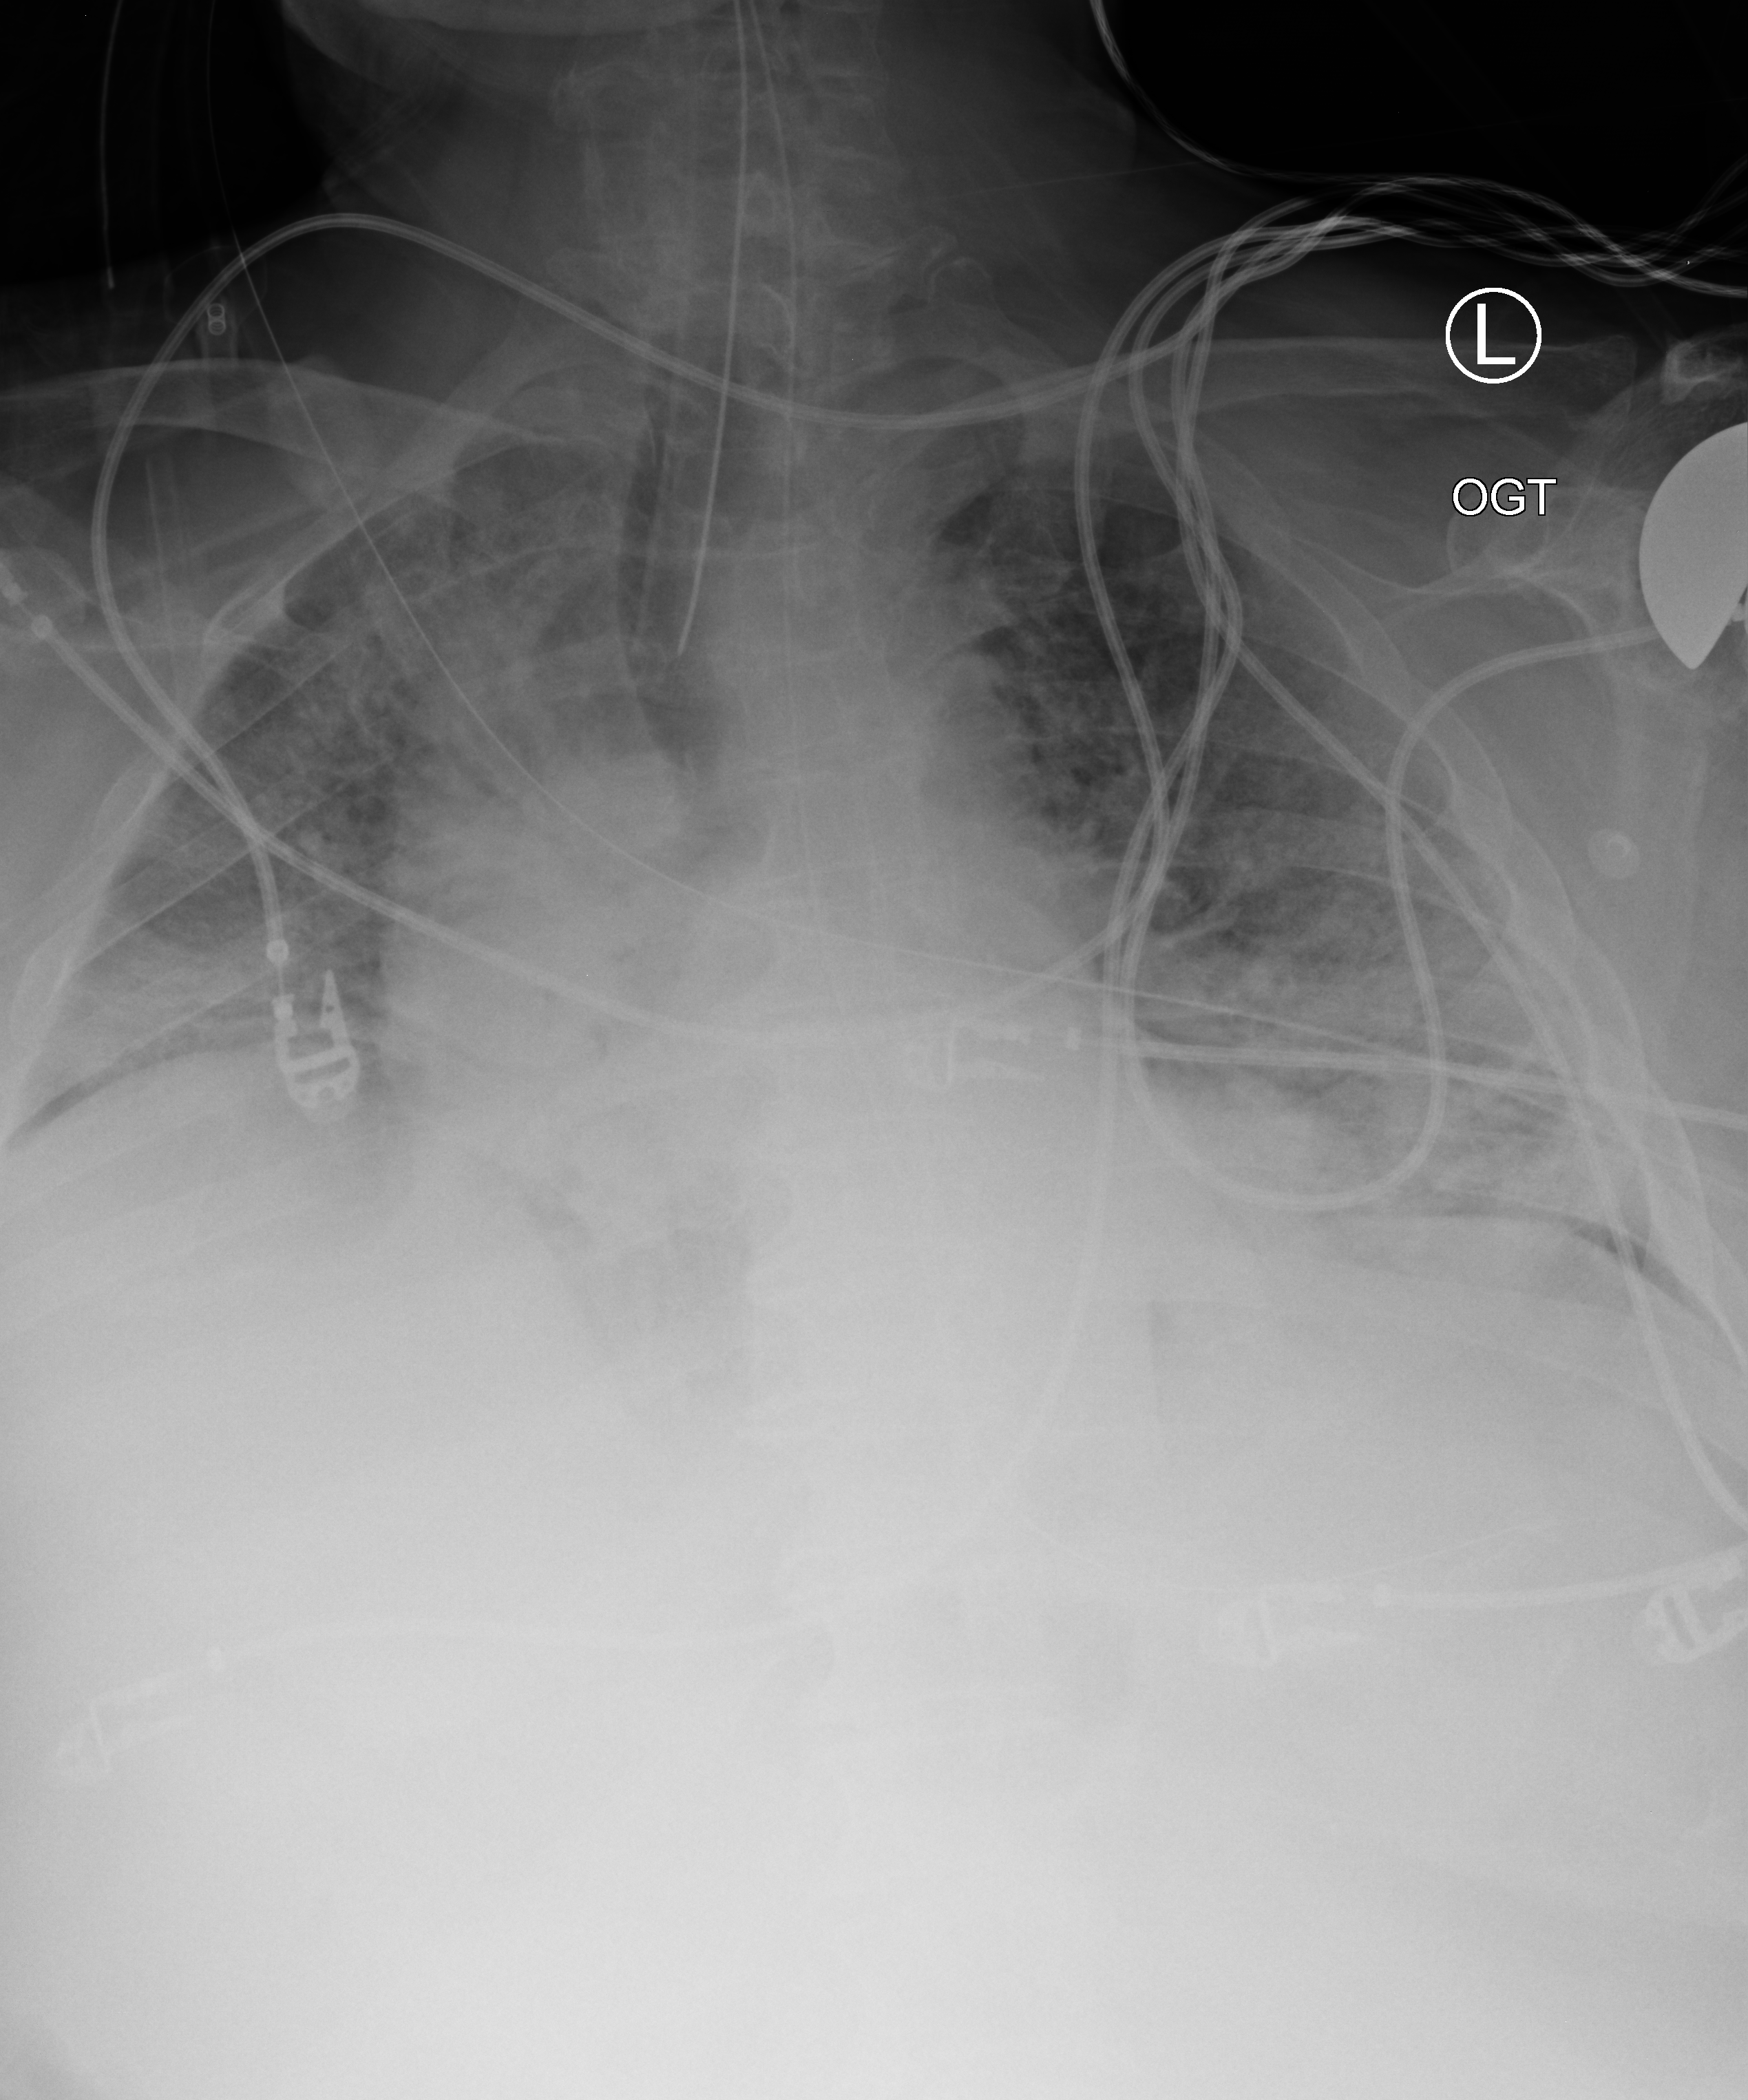
Bedside chest radiograph (computed radiography); anteroposterior (AP) projection. Male patient hospitalised with COVID-19, age 60–74 years.
From the hospital-stay record, not from the radiograph (when in the stay this image was taken is not recorded): other chronic lung disease (admission record): no.